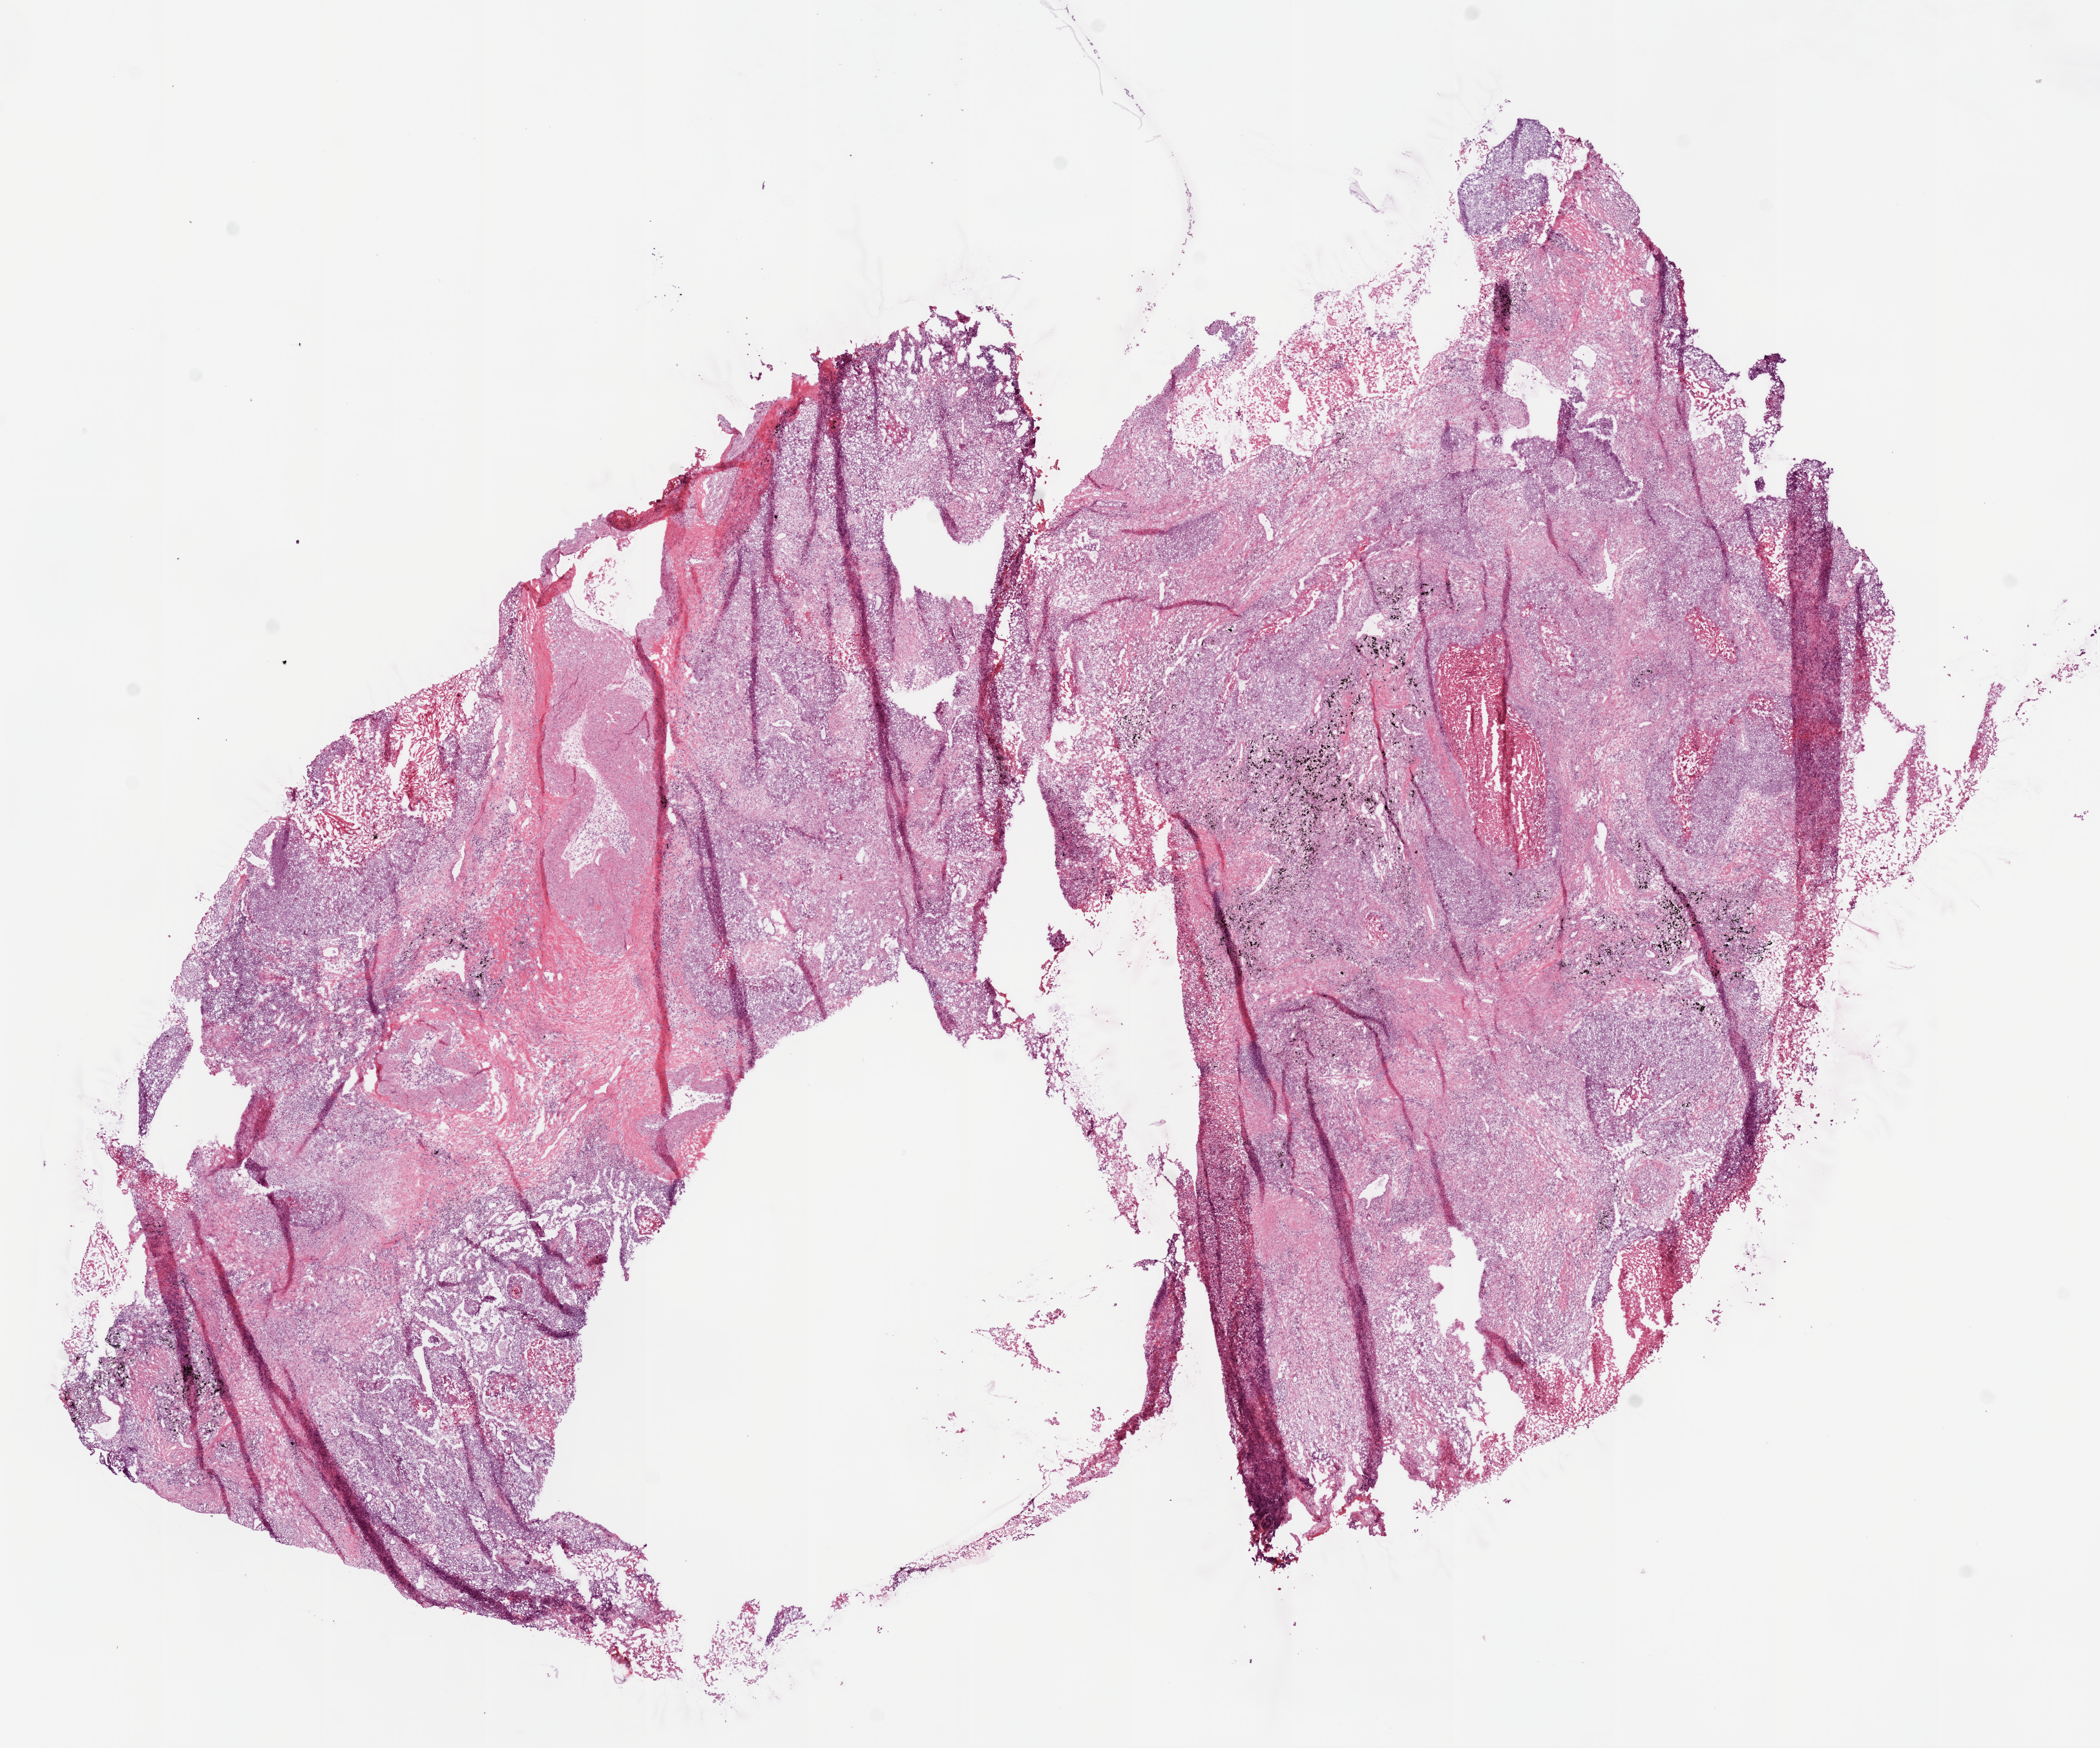
Whole-slide histology image, Hematoxylin and eosin (H&E) stained, shown as a low-resolution overview of the whole scanned area (about 13.0 x 10.9 mm); frozen section from the bottom of the tissue portion; sample: primary tumour, lung. Male, age 70 years at initial diagnosis. Pathologist review of this section (percent, as recorded): tumour cells 64%, tumour nuclei 50%, normal cells 0%, stromal cells 24%, necrosis 12%. Inflammatory infiltration, as recorded: lymphocyte infiltration 20%, monocyte infiltration 2%, neutrophil infiltration 10%.
- AJCC pathologic stage: IB (7th edition)
- histologic diagnosis: Squamous cell carcinoma, NOS (upper lobe, lung)